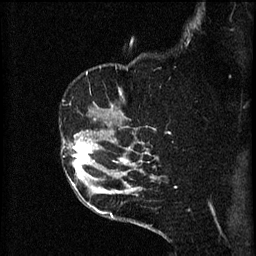
Breast MRI (dynamic contrast-enhanced), one sagittal slice. Position 44 of 60 along the scan axis. 3 images stored at this slice position (order not interpretable as contrast timing). 1.5 T. TE 4.2 ms, TR 8.2 ms. 256 × 256 image matrix, field of view 180 × 180 mm. Patient: female, 49 years.
Annotated regions visible in this slice (semi-automatically segmented with operator editing):
- analysis volume of interest (the breast-tissue region the enhancement analysis was run in; not a lesion): box from (x=62, y=130) to (x=105, y=177) px
- tumour enhancement mask (voxels above the 70 % enhancement threshold inside the analysis volume of interest): (x=63, y=134)–(x=99, y=177)